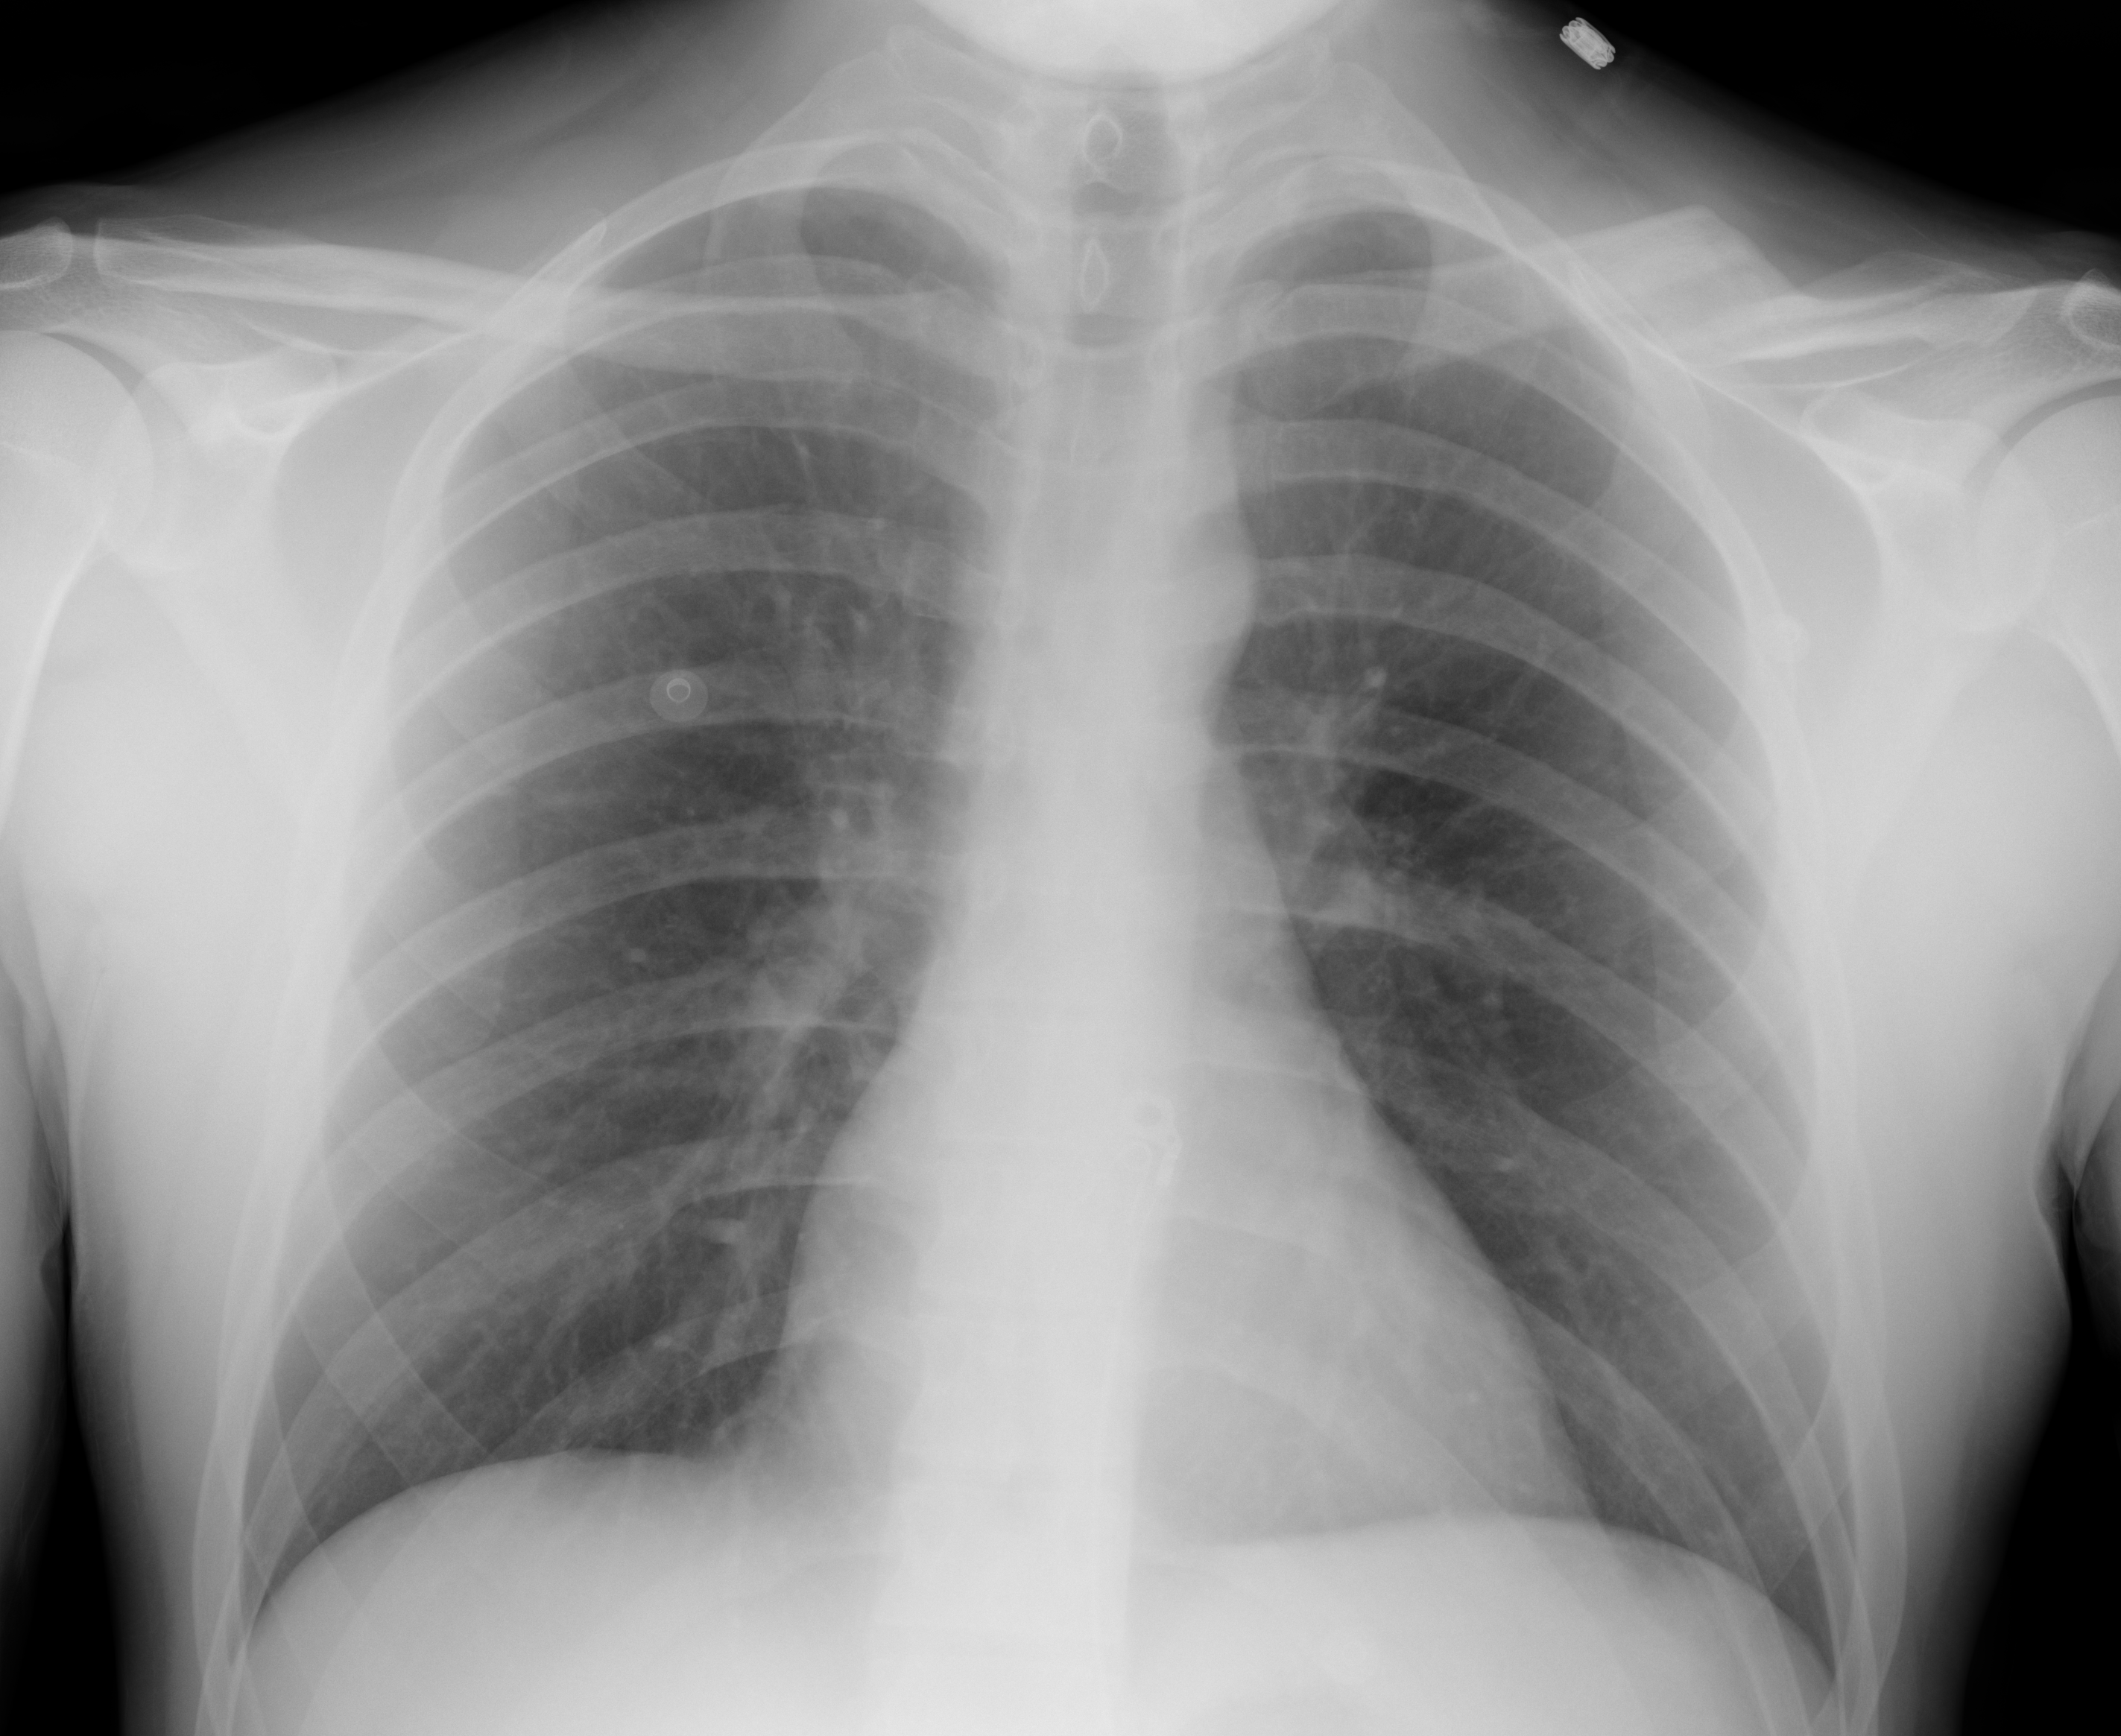
Chest X-ray (portable), AP projection. Male patient, age 26 years; imaged 6 days before the COVID-19 diagnosis.
Radiologist's key findings for this exam: The lungs are well-aerated with no evidence of pneumonic infiltration or pleural effusion.